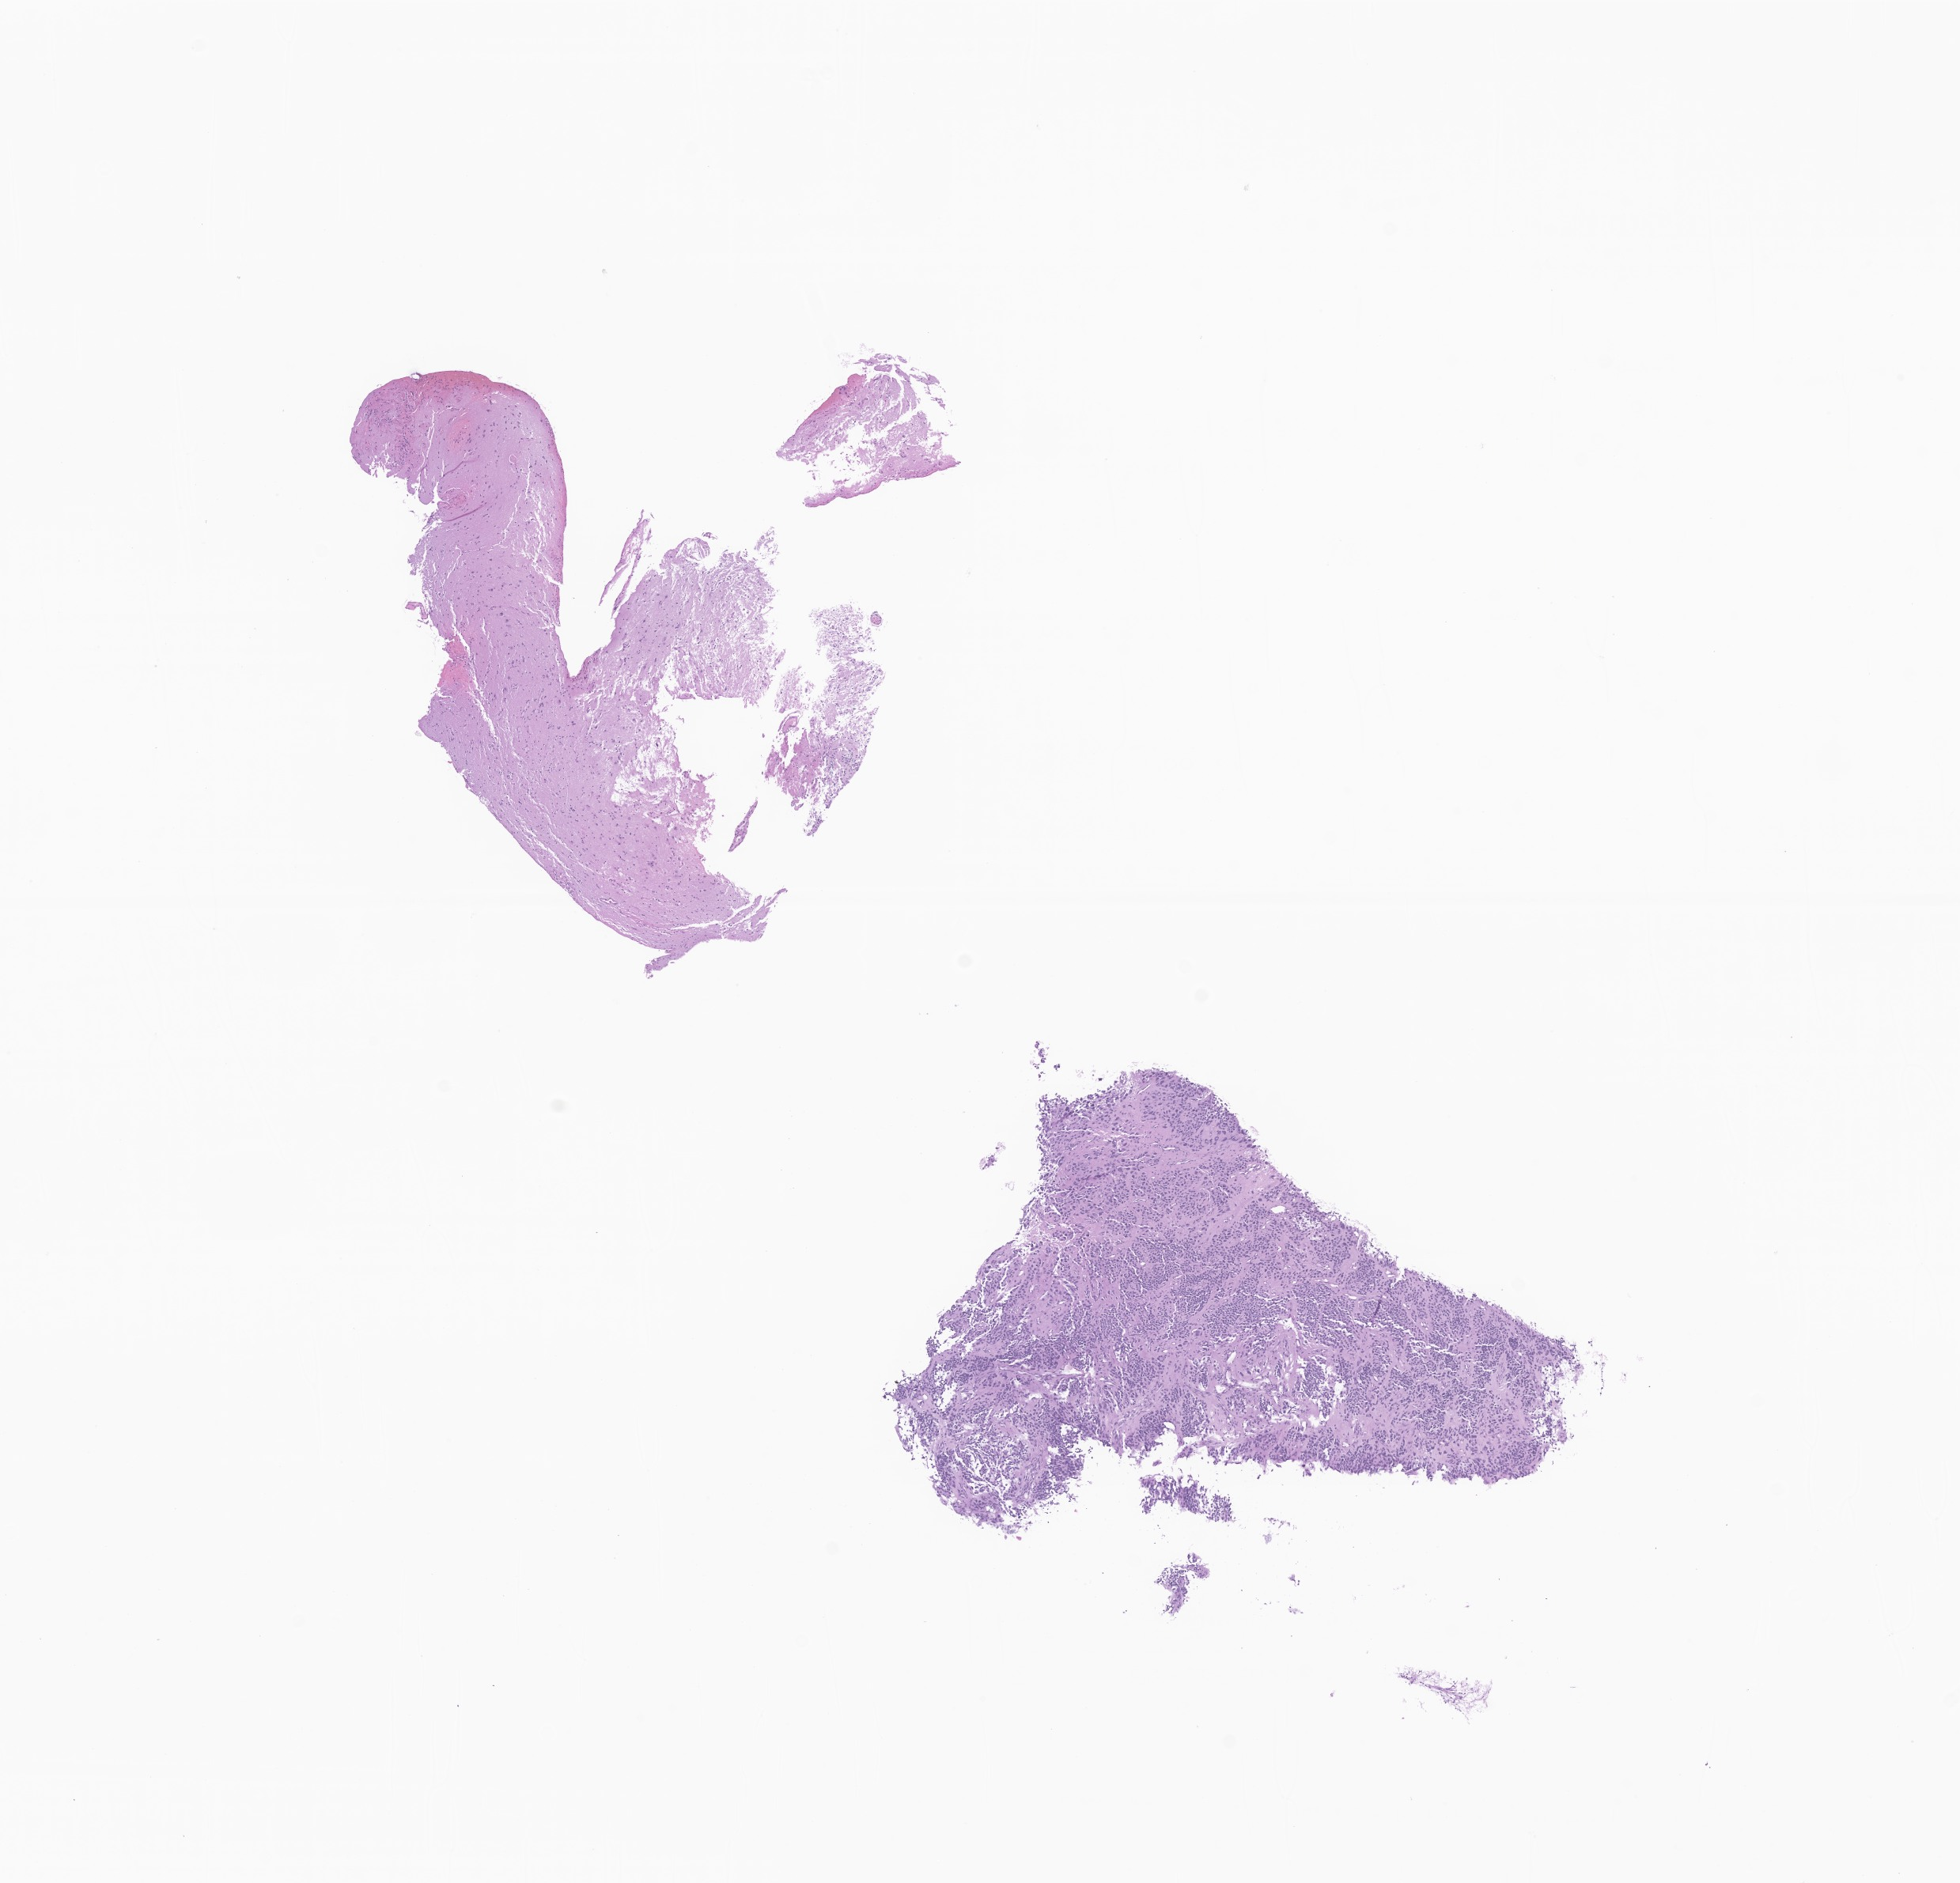
H&E whole-slide image of tumor tissue from the frontal lobe — shown as a low-resolution overview of the whole scanned area (about 10.4 x 10.0 mm); formalin-fixed paraffin-embedded section. Patient female; age 271 months (22 years 7 months).
- recorded diagnosis: Neoplasm, malignant